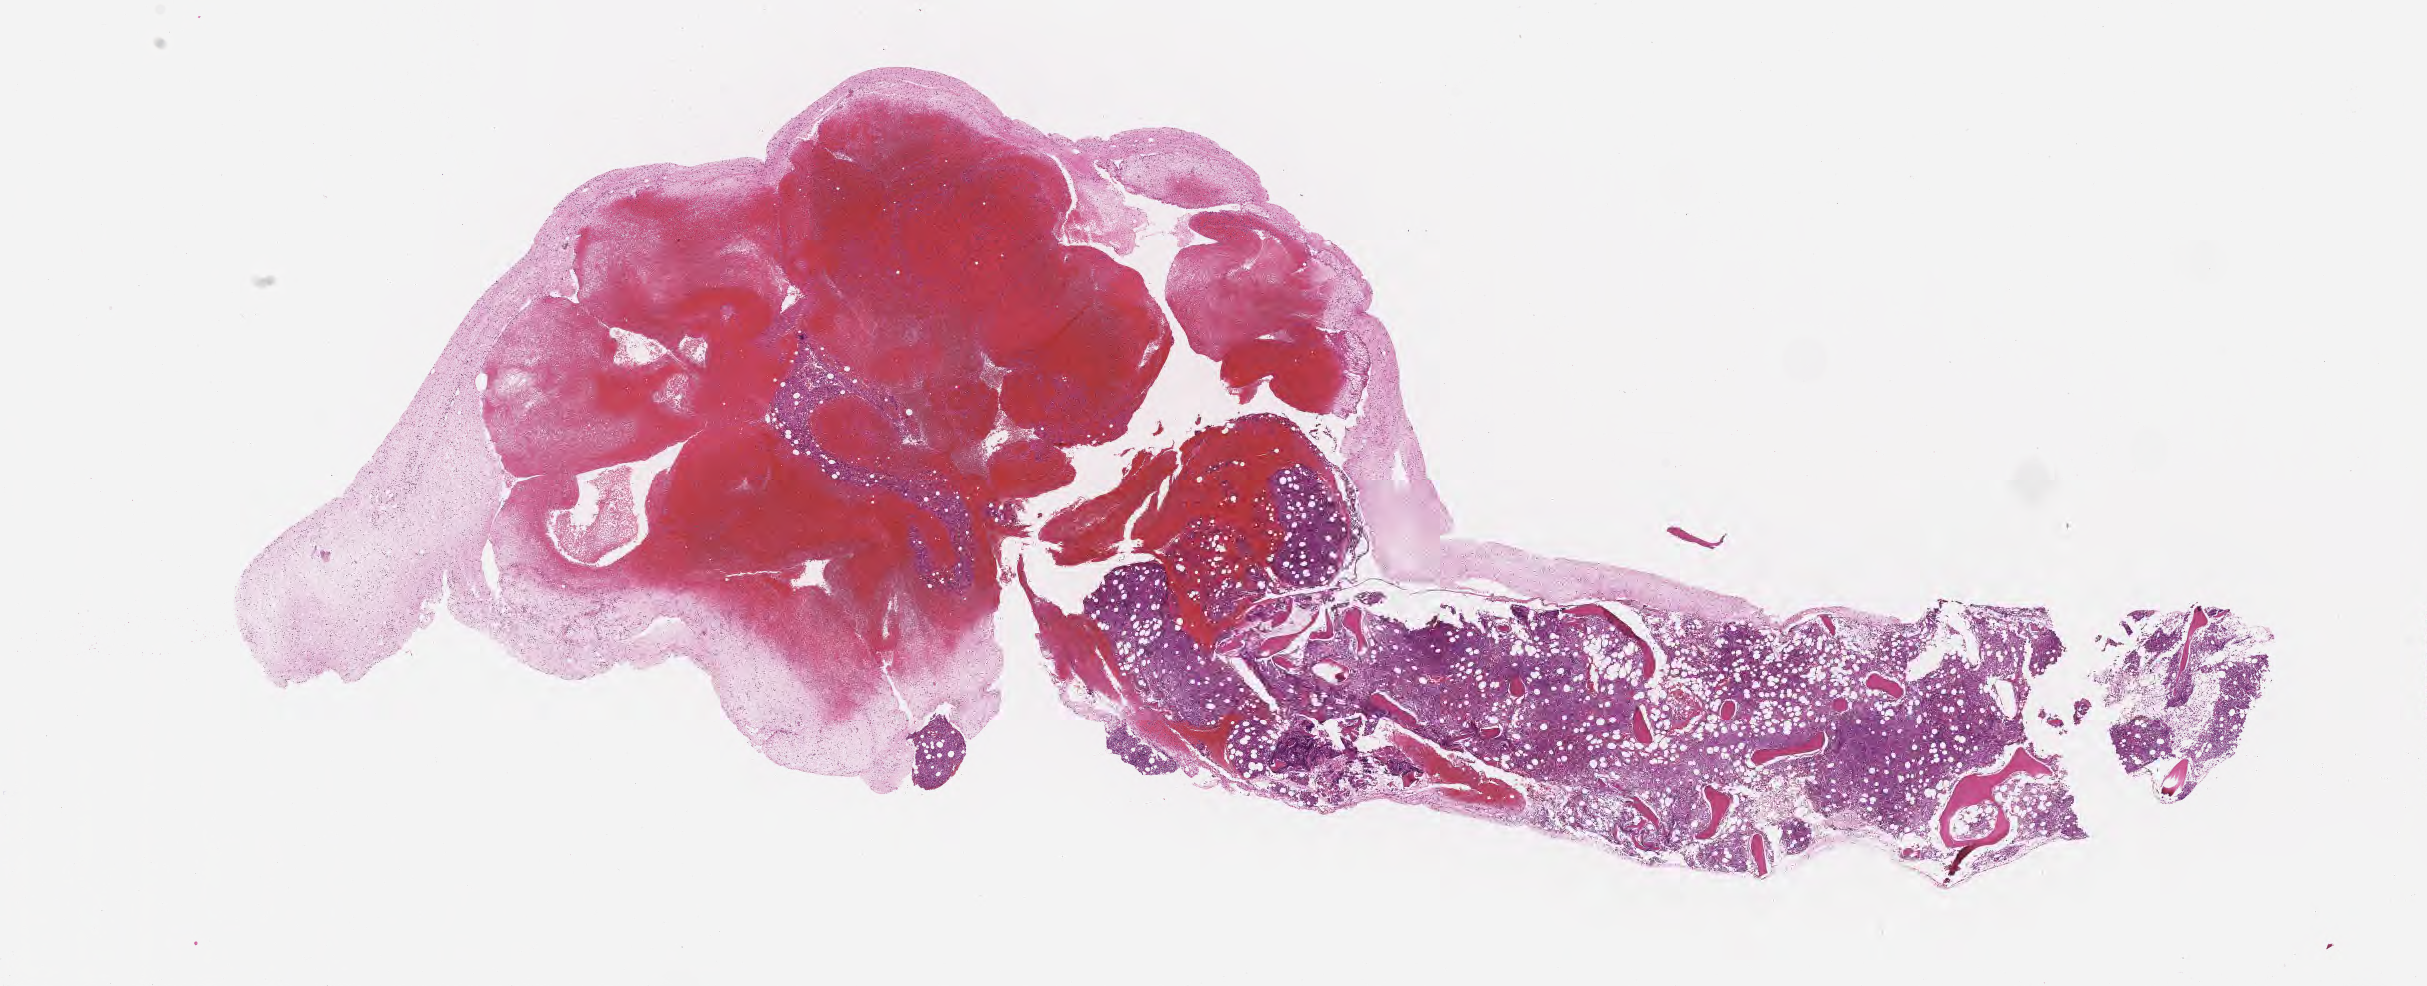
Whole-slide image, hematoxylin and eosin (H&E) stain — shown as a low-resolution overview of the whole scanned area (about 19.6 x 8.0 mm). FFPE section. Specimen: non-tumor (normal tissue) sample from a patient with burkitt lymphoma, NOS. Female patient, age 45 years. Slide review estimates, as recorded: tumor cells 0%, tumor nuclei 0%.
This section: non-tumor tissue sample; the patient's diagnosis is given above. Section: bottom of the tissue portion.